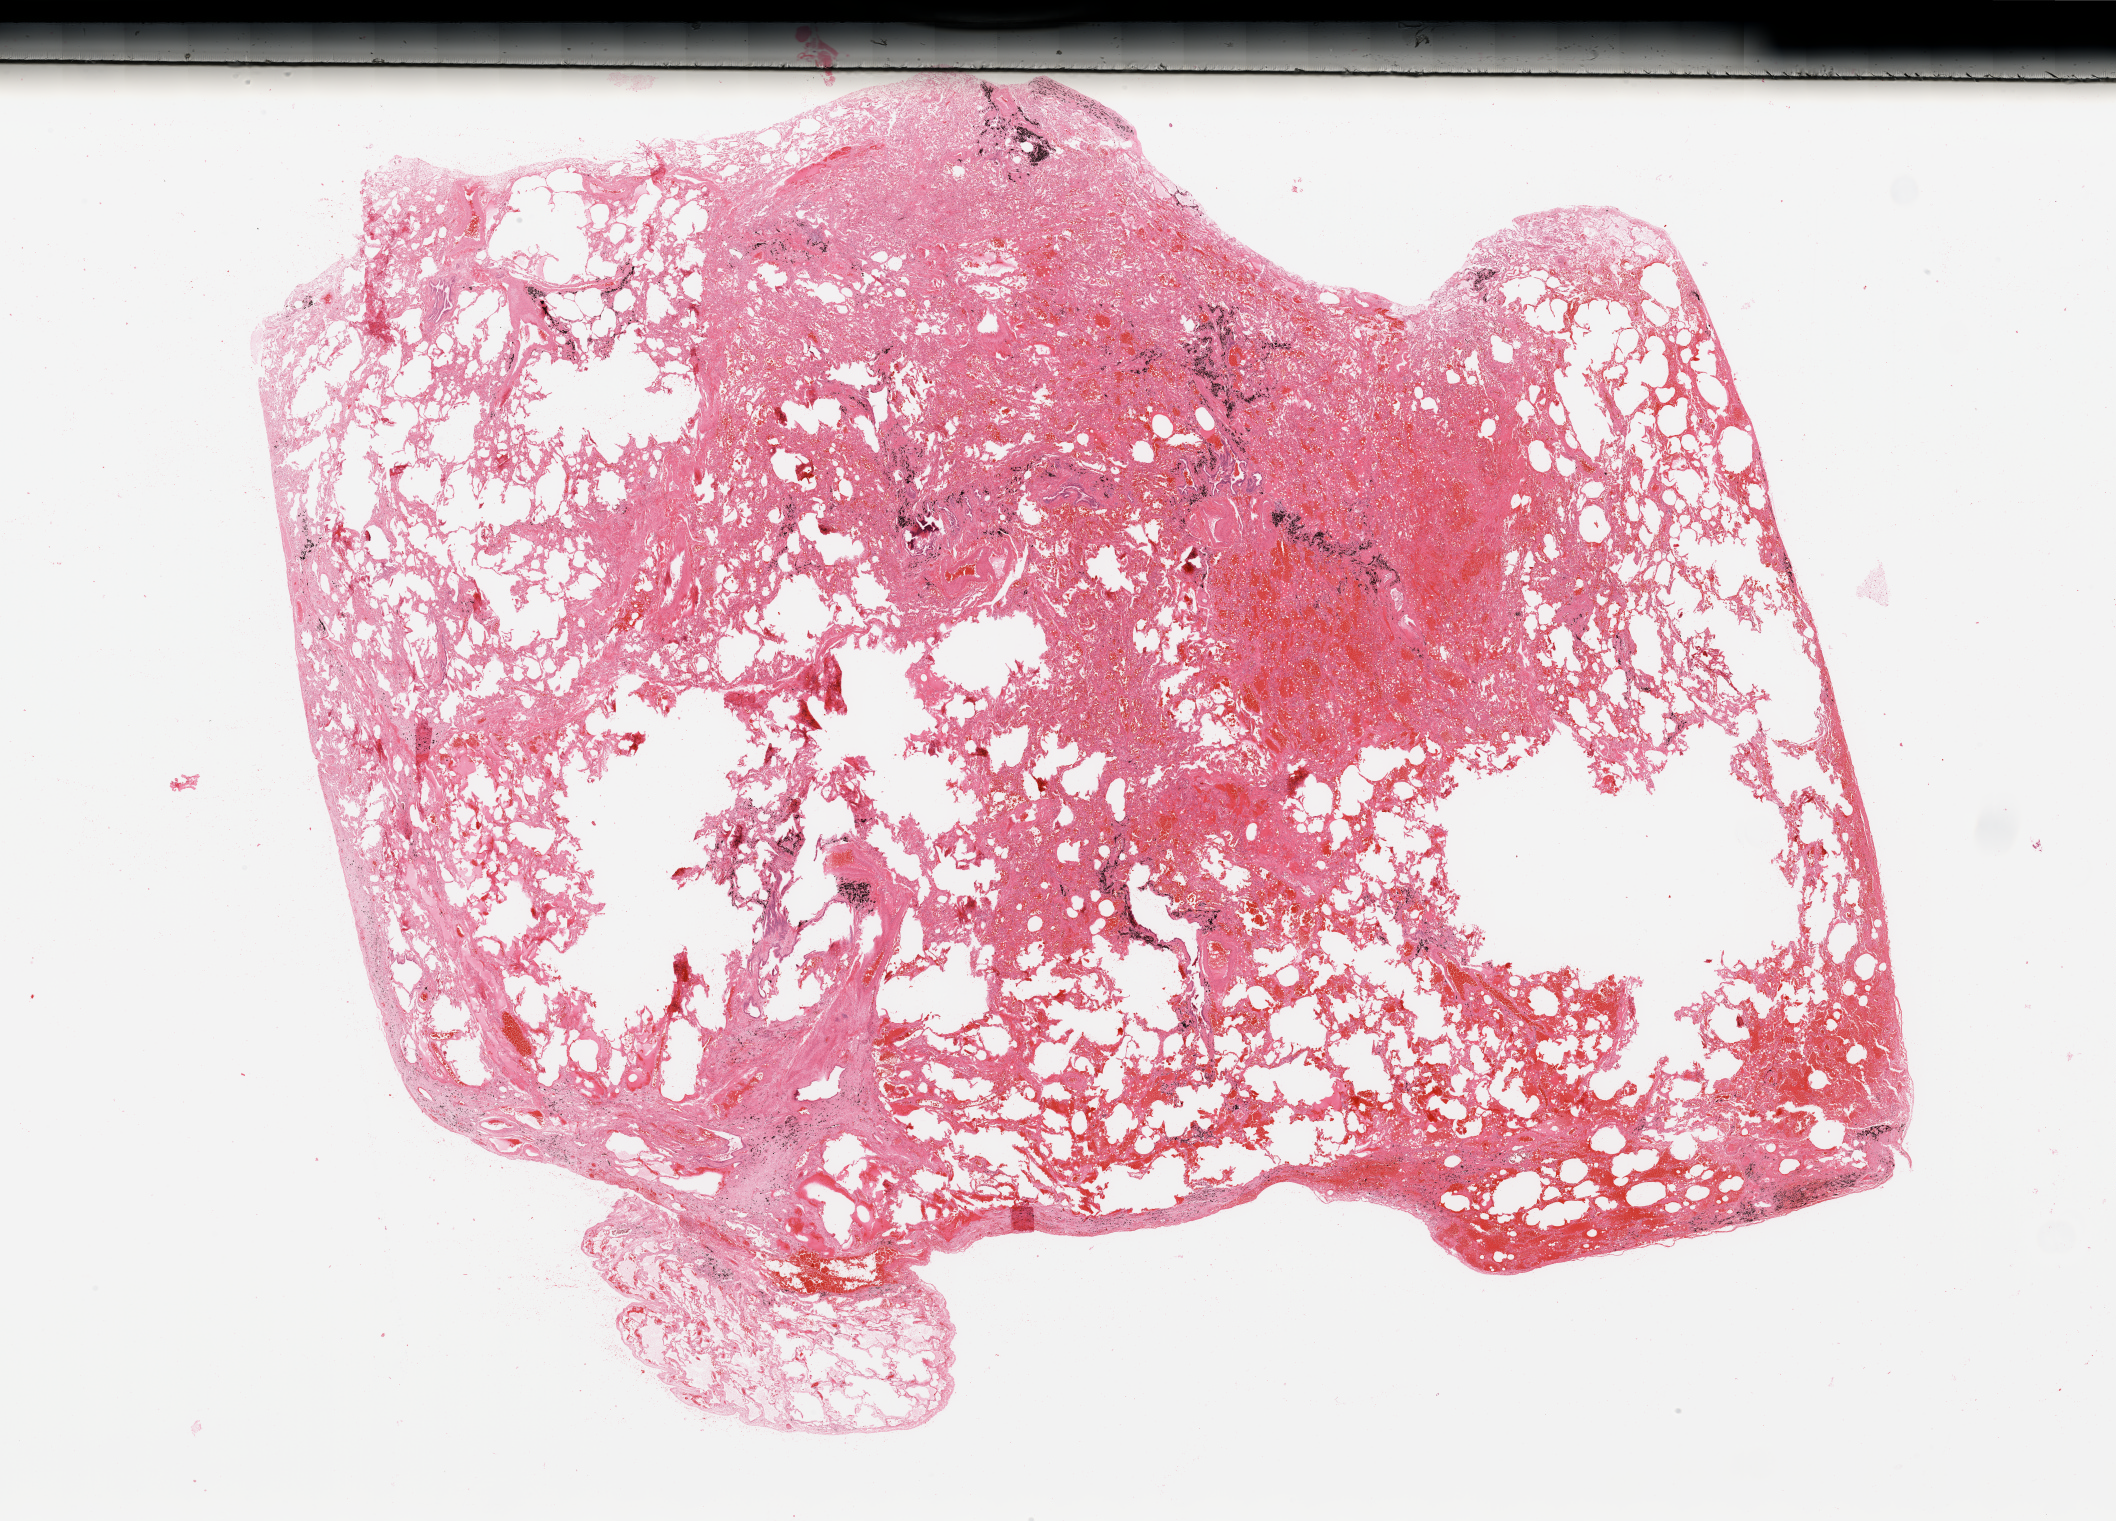
Hematoxylin and eosin (H&E) stained whole-slide image, shown as a low-resolution overview of the whole scanned area (about 33.5 x 24.1 mm), lung, normal (non-tumour) tissue. 63-year-old male patient.
This section: normal (non-tumour) tissue from the same patient. Patient diagnosis: Adenocarcinoma, NOS.